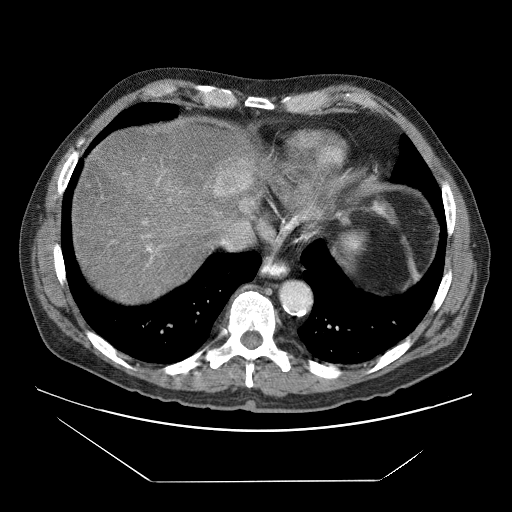
Contrast-enhanced abdominal CT (liver protocol), one axial slice; slice 65 of 83 in the series (ordered by position); reconstruction kernel STANDARD; 120 kVp; soft-tissue window (W 400 / L 40 HU); 2.5 mm slice thickness; 512 × 512 image matrix, field of view 420 × 420 mm. From the clinical record (not read from this slice): diagnosis: hepatocellular carcinoma (patient treated with transarterial chemoembolisation; whether this scan precedes or follows treatment is not stated here); TNM stage (as recorded): Stage-IVB; Child-Pugh class: B; tumour differentiation: poorly differentiated; tumour nodularity: uninodular.
Outlined on this slice (semi-automatically segmented with operator editing):
- liver parenchyma outside the tumour (the mass and vessels are separate outlines, so this box may not span the whole liver): bounding box [x1, y1, x2, y2] px = [72, 121, 254, 302]
- mass: [214, 163, 257, 213]
- liver vessels: [143, 161, 245, 266]